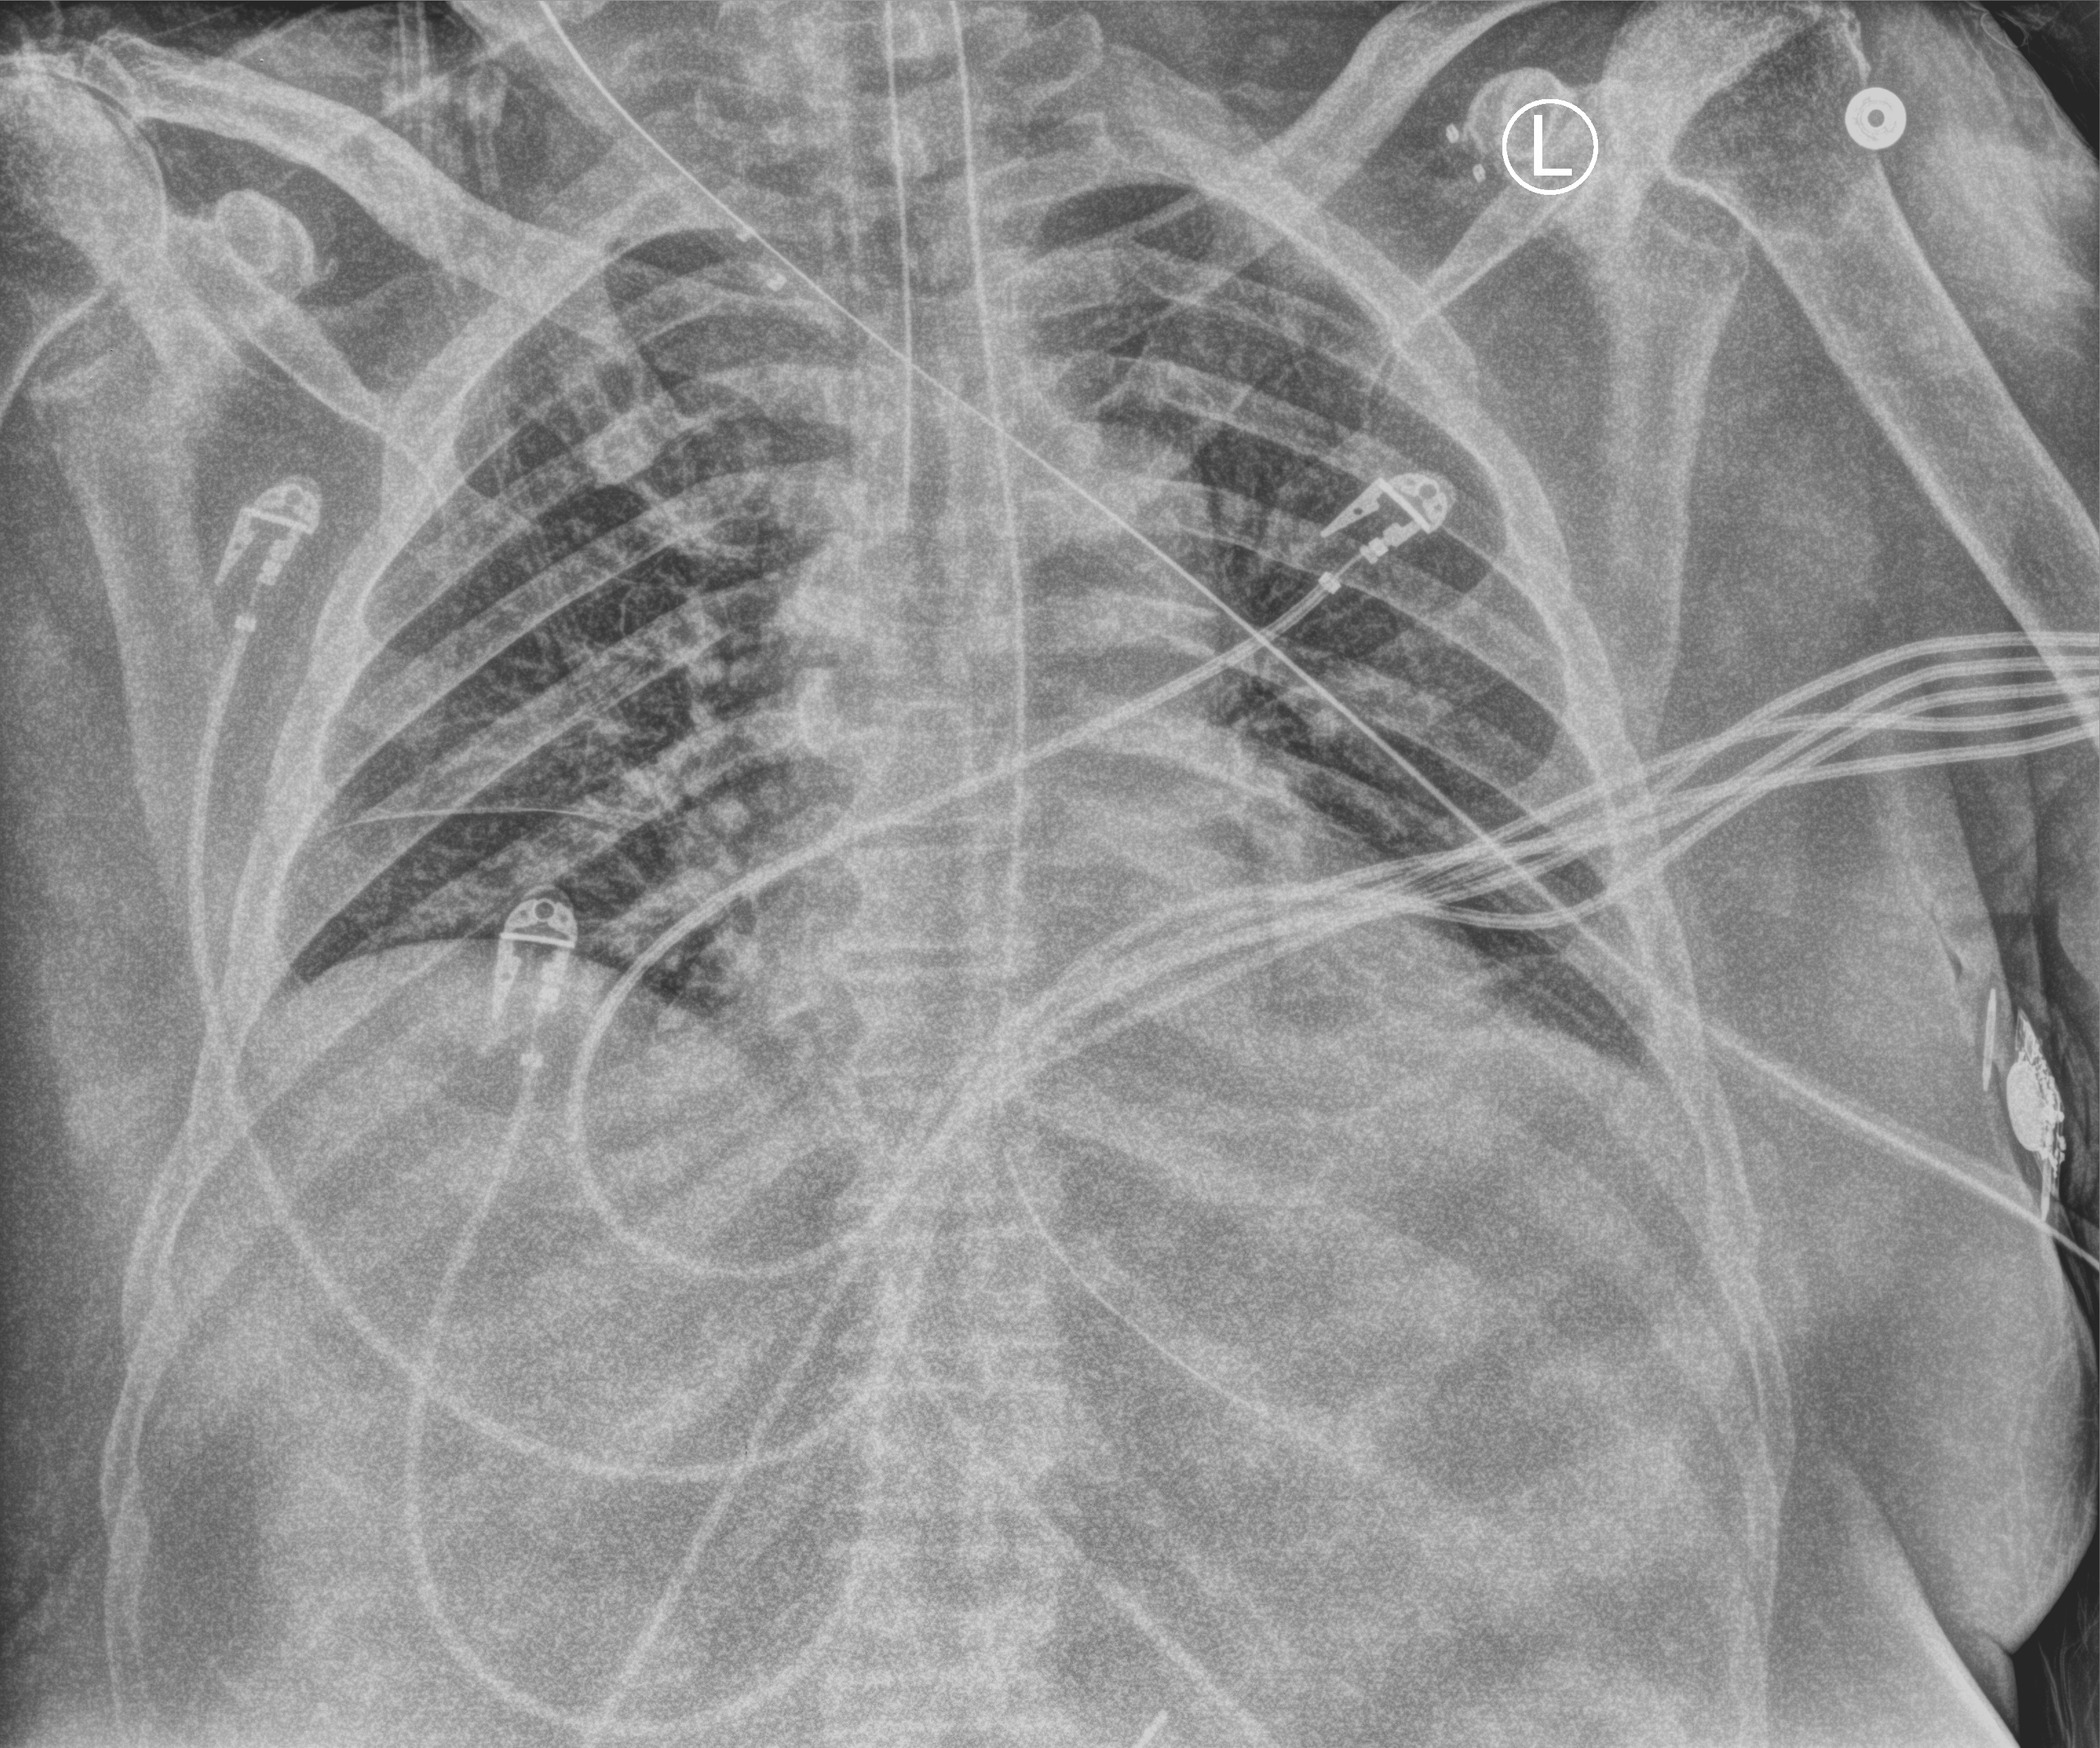
Bedside chest radiograph (computed radiography), anteroposterior (AP) projection. Patient hospitalised with COVID-19; male, aged 75–90 years.
Admission-level facts for this patient (not findings on this image; timing relative to this image not recorded):
- admitted to intensive care during this hospital stay: yes
- chronic kidney disease (admission record): no